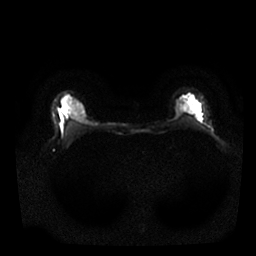
Breast MRI, one axial slice; diffusion-weighted series; image 2 of 4 stored at this slice position (different b-values; order by instance number); 1.5 T; 4 mm slice thickness; 256 × 256 image matrix, field of view 320 × 320 mm. Female patient.
Structures marked on this image (outlined manually by an expert reader):
- tumour on diffusion-weighted imaging: bounding box <177,109,181,113> (left, top, right, bottom; pixels)